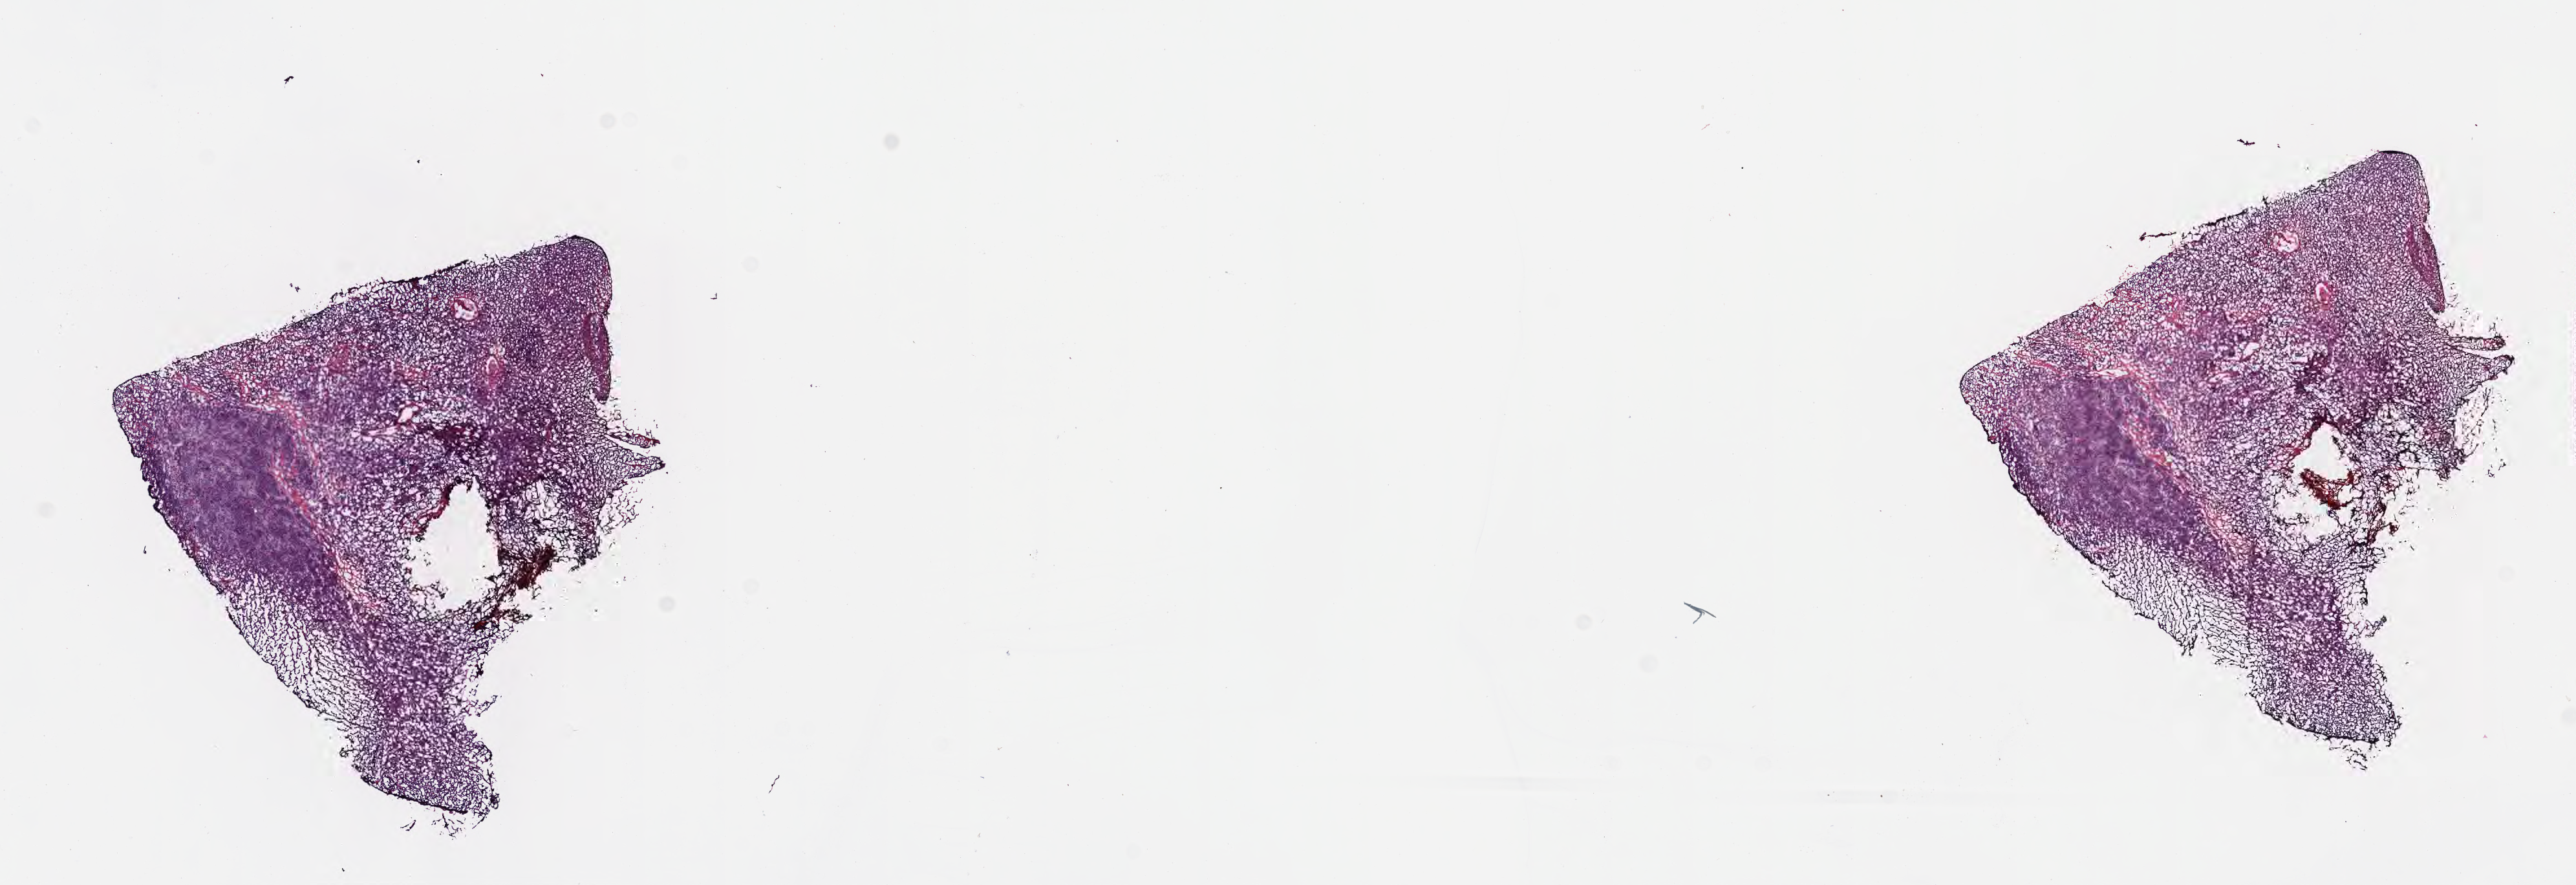
Whole-slide image, H&E stain, whole scanned area (about 16.1 x 5.5 mm) shown as a low-resolution overview. Frozen section (tissue freezing medium). Specimen: primary tumor. Site: mandible. Male patient; age at initial diagnosis 6 years. Composition of this section per pathologist review: tumor cells 30%, tumor nuclei 50%, stromal cells 70%, necrosis 0%, normal cells 0%. Infiltration values recorded for this section: lymphocyte infiltration 80%, monocyte infiltration 5%, neutrophil infiltration 5%.
Ann Arbor stage (patient): Stage IV. Diagnosis: Diffuse large B-cell lymphoma, NOS.